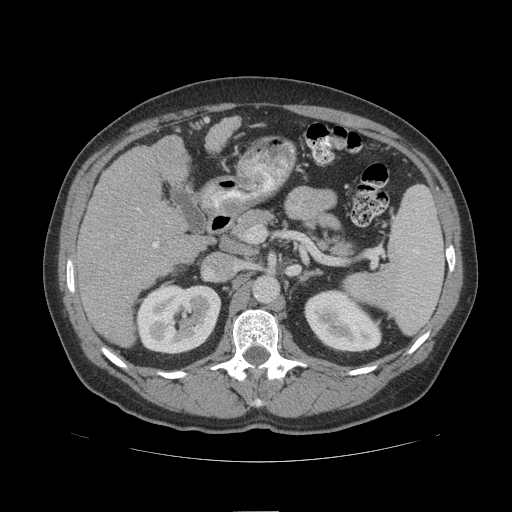
Contrast-enhanced abdominal CT (liver protocol), one axial slice; position 56 of 109 along the scan axis; reconstruction kernel STANDARD; 140 kVp; soft-tissue window (W 400 / L 40 HU); 2.5 mm slice thickness; 512 × 512 image matrix, field of view 420 × 420 mm. Case-level facts recorded for this patient, not image findings: diagnosis: hepatocellular carcinoma (patient treated with transarterial chemoembolisation; whether this scan precedes or follows treatment is not stated here); TNM stage (as recorded): Stage-IIIB; Child-Pugh class: A; tumour differentiation: poorly differentiated.
Structures marked on this image (semi-automatic segmentation, software-assisted and operator-edited):
- liver parenchyma outside the tumour (the mass and vessels are separate outlines, so this box may not span the whole liver): bounding box <76,116,240,346> (left, top, right, bottom; pixels)
- liver vessels: <152,242,158,248>